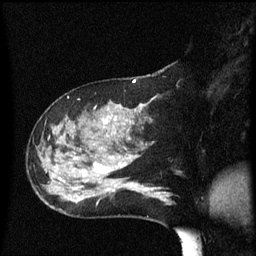
Breast MRI (dynamic contrast-enhanced), one sagittal slice. Position 25 of 60 along the scan axis. Dynamic contrast-enhanced series, image 2 of 3 at this slice position (ordered by acquisition). 1.5 T. TE 4.2 ms, TR 8.4 ms. 256 × 256 image matrix, field of view 200 × 200 mm. Patient: female, 47 years.
Structures marked on this image (semi-automatically segmented with operator editing):
- analysis volume of interest (the breast-tissue region the enhancement analysis was run in; not a lesion): bounding box (x1, y1, x2, y2) in pixels: (36, 104, 149, 206)
- tumour enhancement mask (voxels above the 70 % enhancement threshold inside the analysis volume of interest): (100, 118, 117, 184)